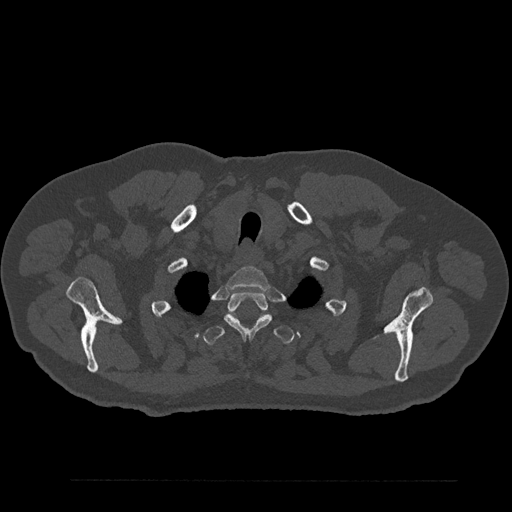
CT including the spine, one axial slice. Slice 715 of 797 in the series (ordered by position). 120 kVp. Bone window (W 1800 / L 400 HU). 0.5 mm slice thickness. 512 × 512 image matrix, field of view 430 × 430 mm. Patient: male, 61 years. From the clinical record (not read from this slice): primary cancer: prostate.
Outlined on this slice (semi-automatically segmented with operator editing):
- T1 vertebra: bounding box <226,267,270,289> (left, top, right, bottom; pixels)
- T2 vertebra: <224,291,272,339>
- T3 vertebra: <204,315,294,345>